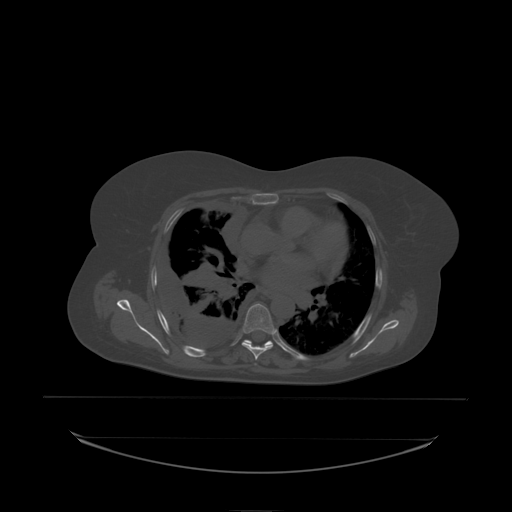
CT including the spine, one axial slice; bone window (W 1800 / L 400 HU); 512 × 512 image matrix. Patient: female, 53 years. From the clinical record (not read from this slice): primary cancer: lung; vertebrae with lytic lesions (as recorded): T7, L1.
Structures marked on this image (semi-automatically segmented with operator editing):
- T6 vertebra: bounding box (x1, y1, x2, y2) in pixels: (243, 304, 276, 336)